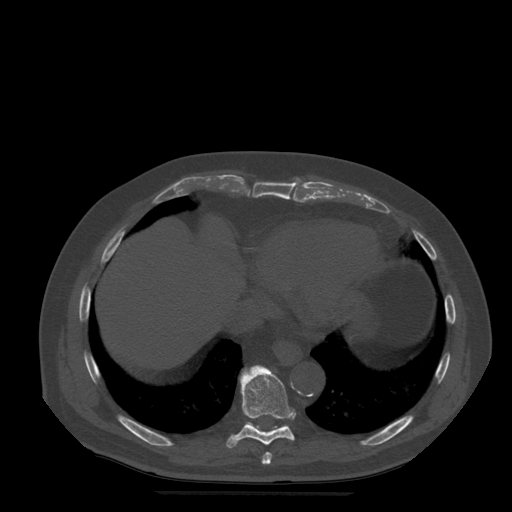
CT including the spine, one axial slice. Position 288 of 522 along the scan axis. Bone window (W 1800 / L 400 HU). 1.25 mm slice thickness. 512 × 512 image matrix, field of view 420 × 420 mm. Patient age 72 years. From the clinical record (not read from this slice): primary cancer: prostate.
Outlined on this slice (semi-automatically segmented with operator editing):
- T8 vertebra: bounding box <262,452,272,465> (left, top, right, bottom; pixels)
- T9 vertebra: <227,365,295,449>